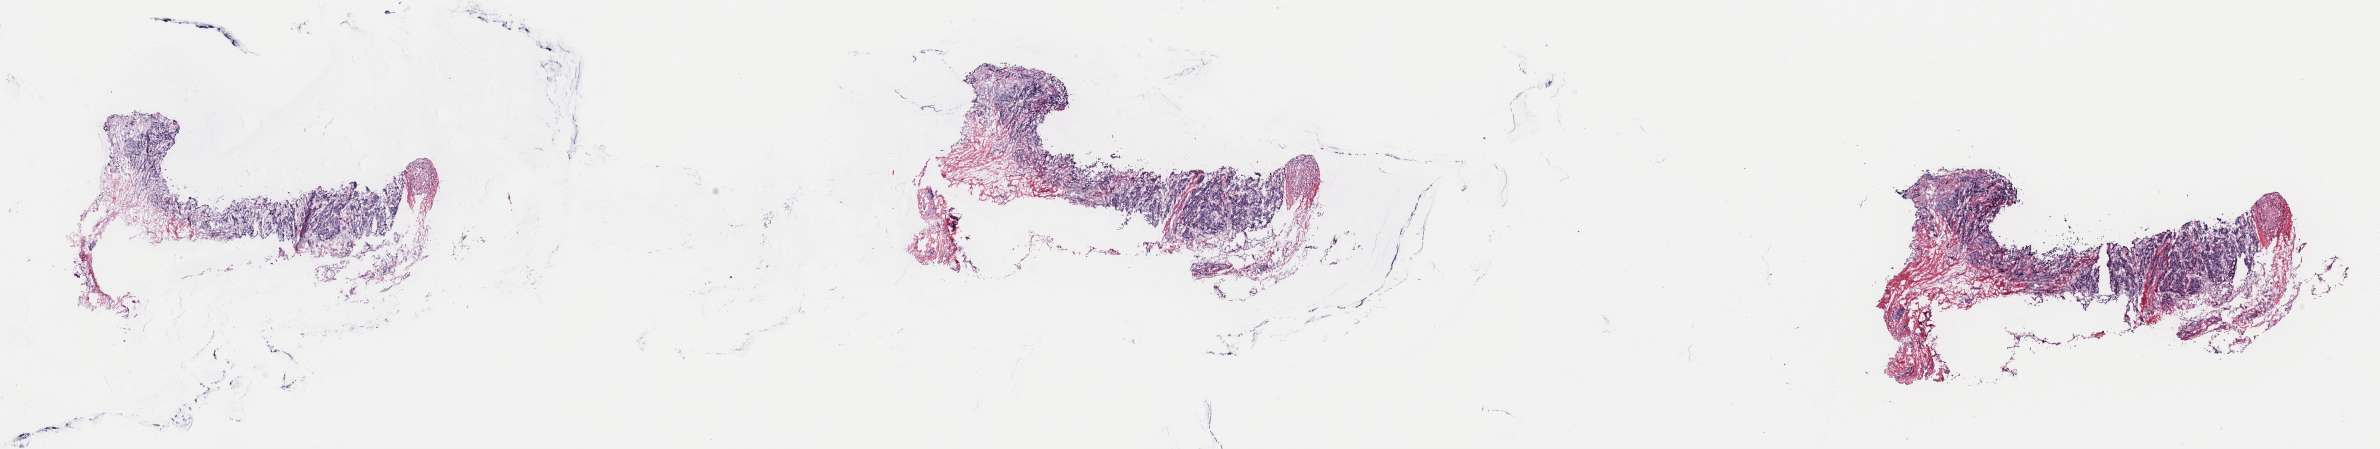
H&E whole-slide image, low-resolution overview of the scanned area, about 37.6 x 7.1 mm (acquisition: 40x scan). Frozen section. Breast, primary tumour sample. Female, age 68 years at initial diagnosis. Slide review estimates, as recorded: tumour cells 60%, tumour nuclei 60%, normal cells 20%, stromal cells 20%, necrosis 0%. Infiltration values recorded for this section: lymphocyte infiltration 5%, monocyte infiltration 1%, neutrophil infiltration 1%.
• AJCC pathologic stage: IIA
• histologic diagnosis: Infiltrating duct carcinoma, NOS
• lymph nodes positive (case pathology): 0 of 2 examined
• laterality: left